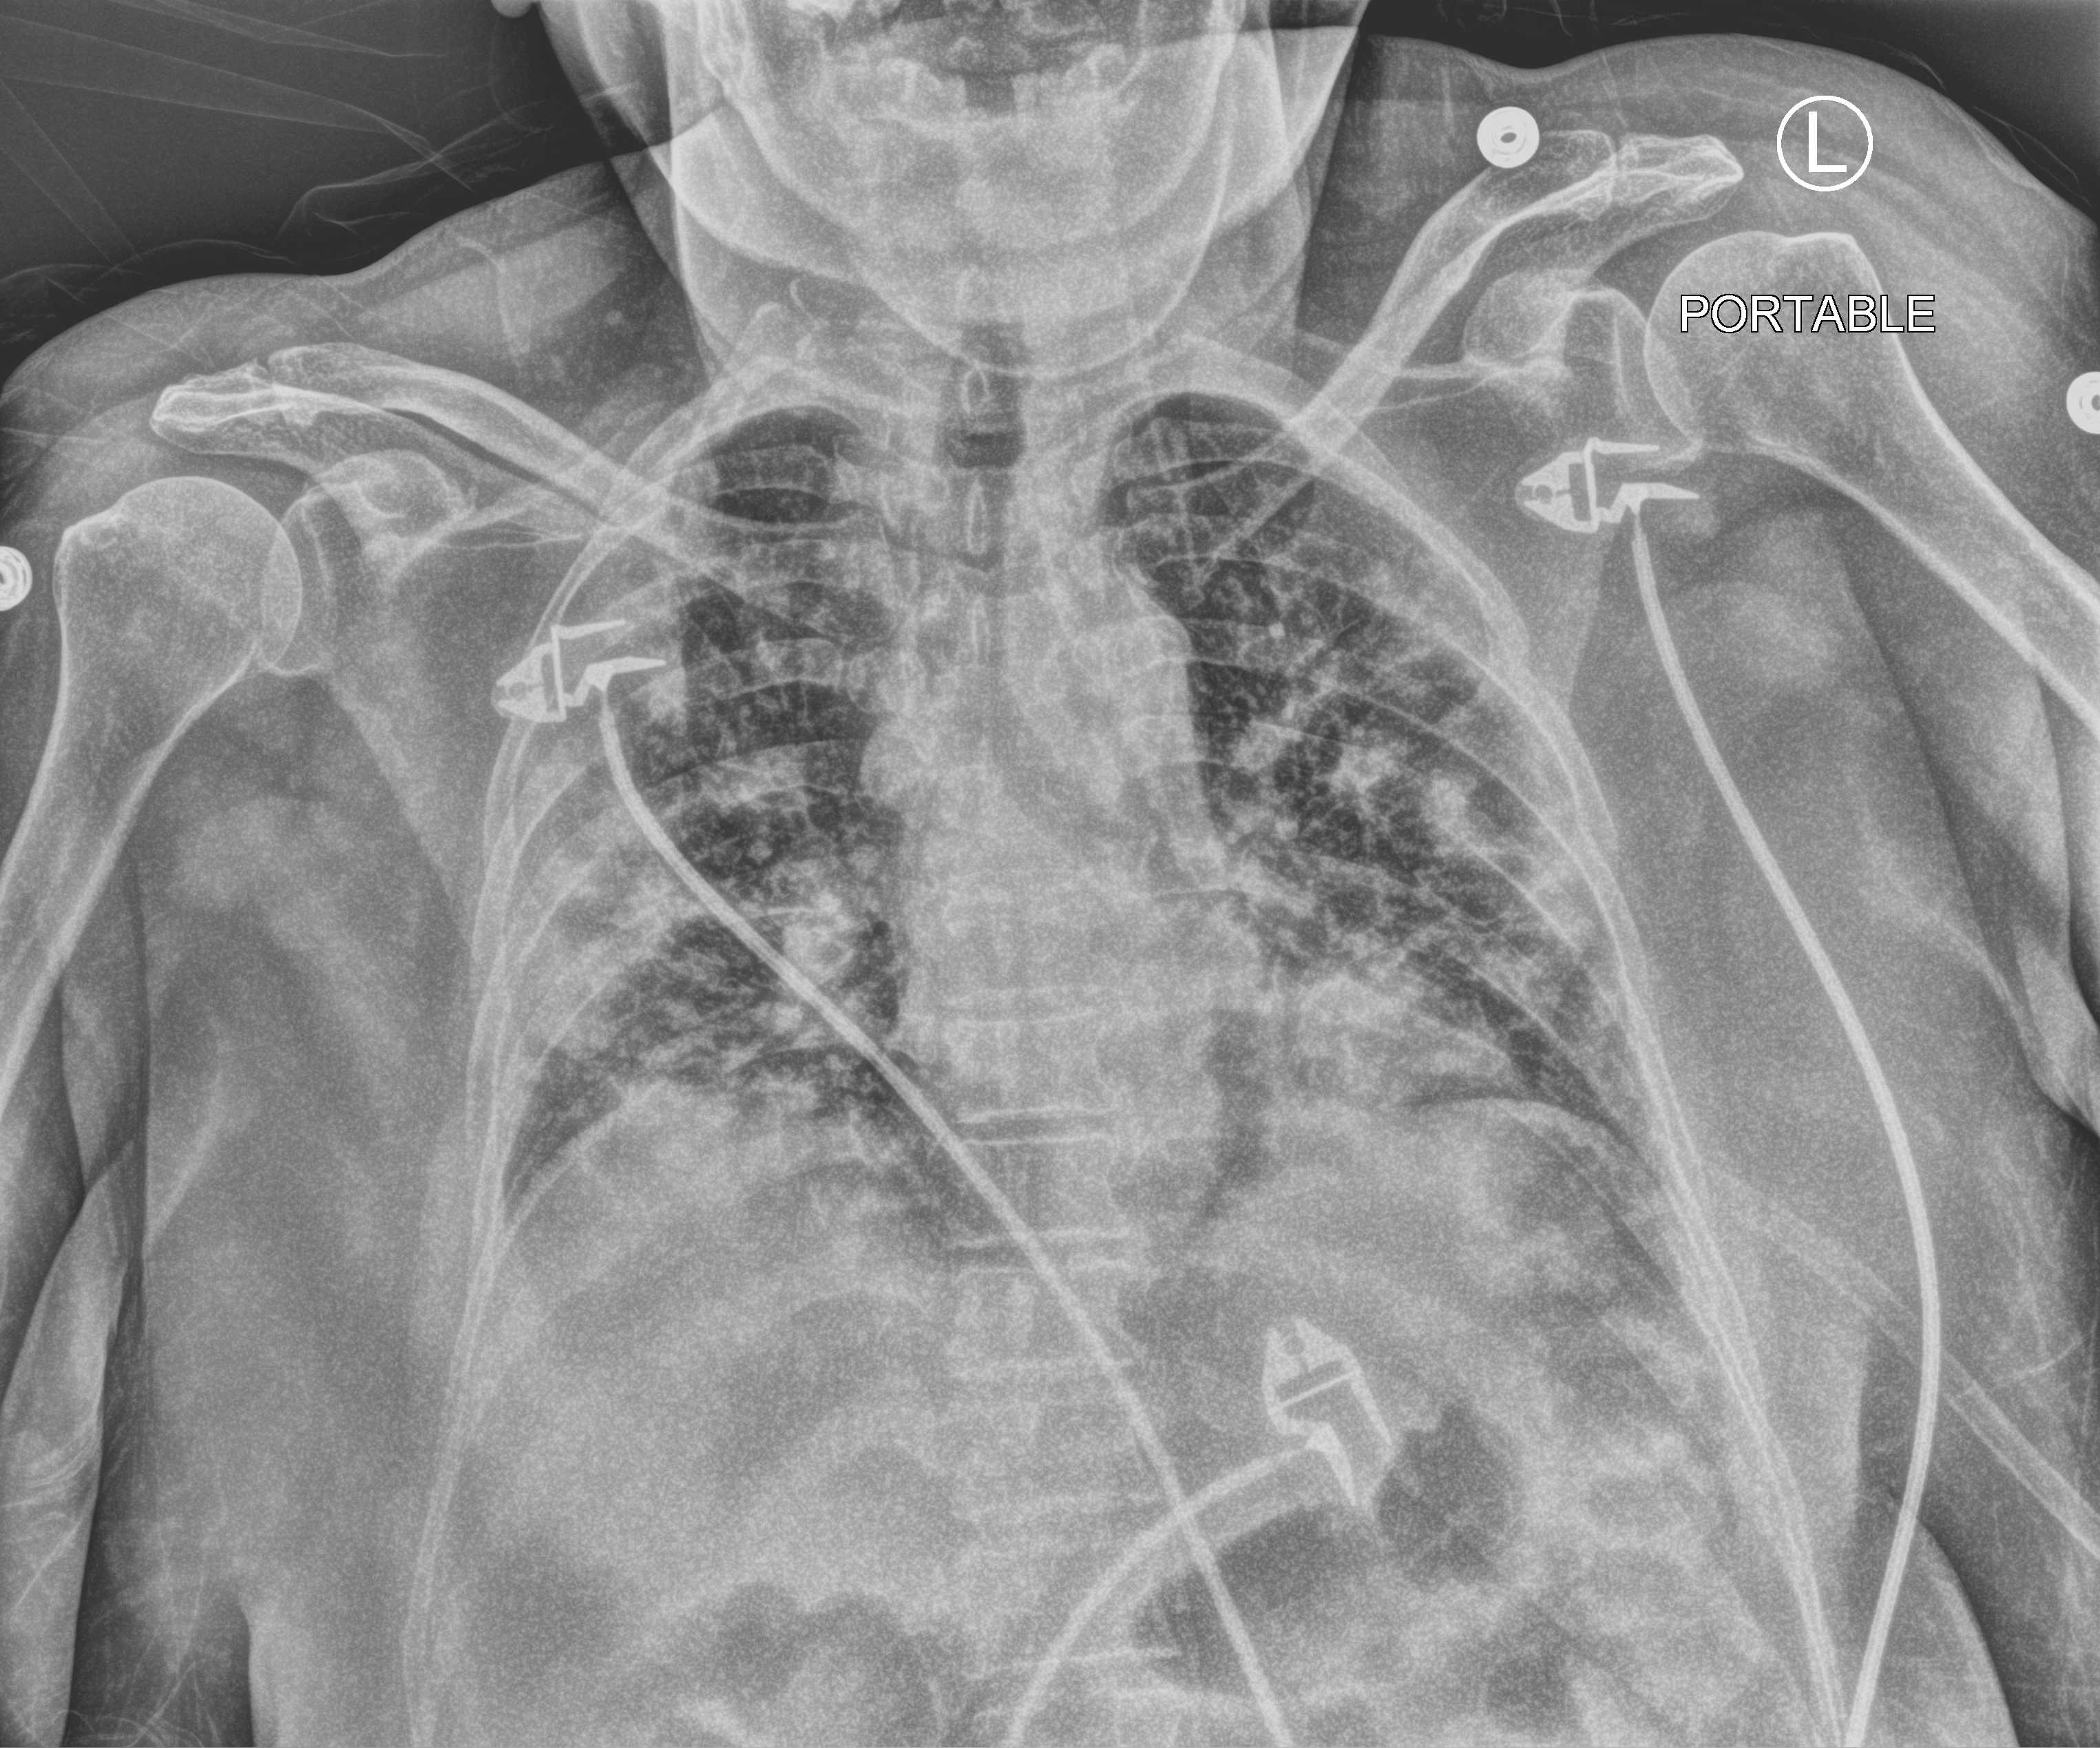
Bedside chest radiograph (computed radiography), anteroposterior (AP) projection. Patient hospitalised with COVID-19; female, aged 60–74 years.
Admission-level facts for this patient (not findings on this image; timing relative to this image not recorded):
- smoking status (admission record): never
- admitted to intensive care during this hospital stay: no
- length of hospital stay: 14 days